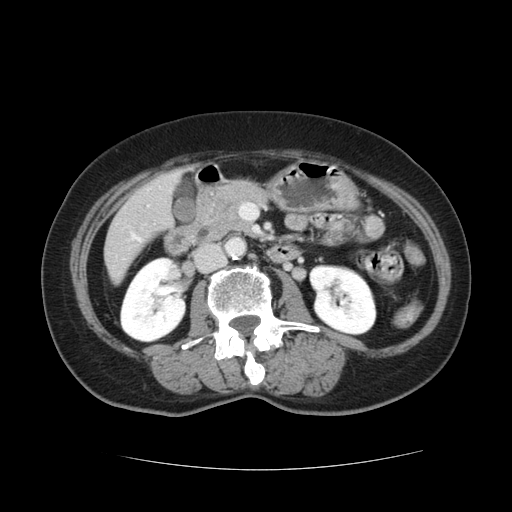
Contrast-enhanced abdominal CT, one axial slice; slice 34 of 128 in the series (ordered by position); 120 kVp; intravenous contrast given; soft-tissue window (W 400 / L 40 HU); 512 × 512 image matrix, field of view 366 × 366 mm. Female patient, age 67 years. Case-level facts recorded for this patient, not image findings: diagnosis: colorectal cancer liver metastases, imaged before liver resection; multiple liver metastases: yes.
Annotated regions visible in this slice (manually delineated by an expert):
- liver: bounding box <105,174,178,279> (left, top, right, bottom; pixels)
- planned liver remnant (the part of the liver to remain after resection): <105,216,142,279>